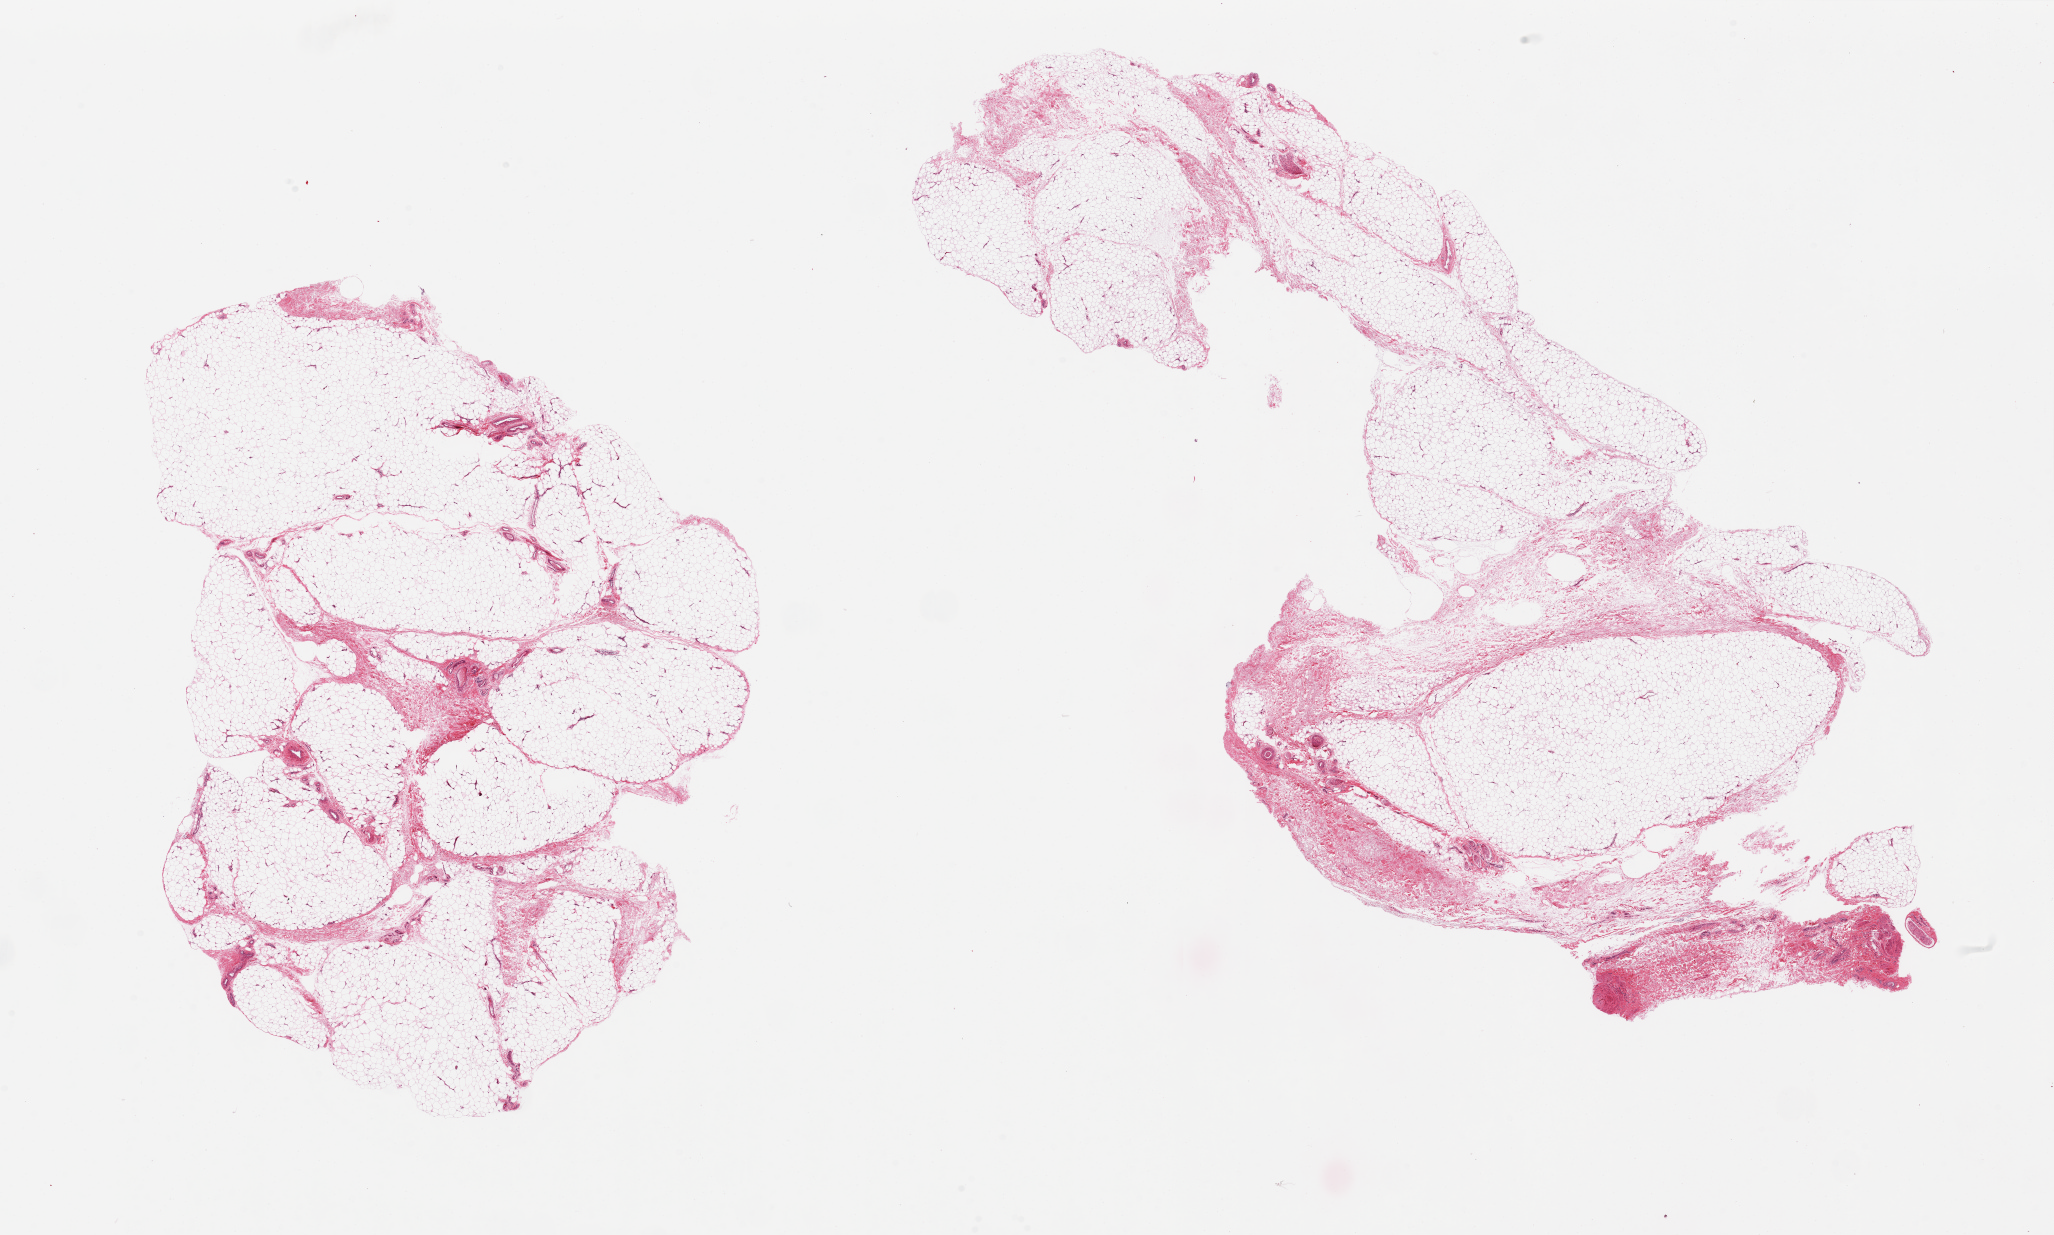
Digitized haematoxylin and eosin-stained section, brightfield, low-resolution overview of the scanned area, about 32.5 x 19.5 mm (slide scanned at 20x), PAXgene-fixed paraffin-embedded (PFPE) section, sampled site (target tissue): adipose tissue, donor tissue sample. Donor sex: male.
Review note (as recorded): 2 pieces, ~10-20% fibrovascular/fascial tissue.